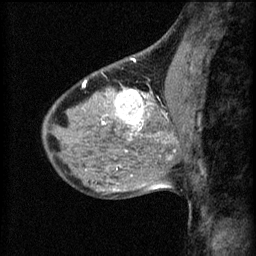
Breast MRI (dynamic contrast-enhanced), one sagittal slice; slice 27 of 60 in the series (ordered by position); 3 images stored at this slice position (order not interpretable as contrast timing); 1.5 T; TE 4.2 ms, TR 8.2 ms; 256 × 256 image matrix. Patient: female, 40 years.
Annotated regions visible in this slice (semi-automatic segmentation, software-assisted and operator-edited):
- analysis volume of interest (the breast-tissue region the enhancement analysis was run in; not a lesion): bounding box [x1, y1, x2, y2] px = [108, 82, 175, 139]
- tumour enhancement mask (voxels above the 70 % enhancement threshold inside the analysis volume of interest): [108, 90, 151, 133]